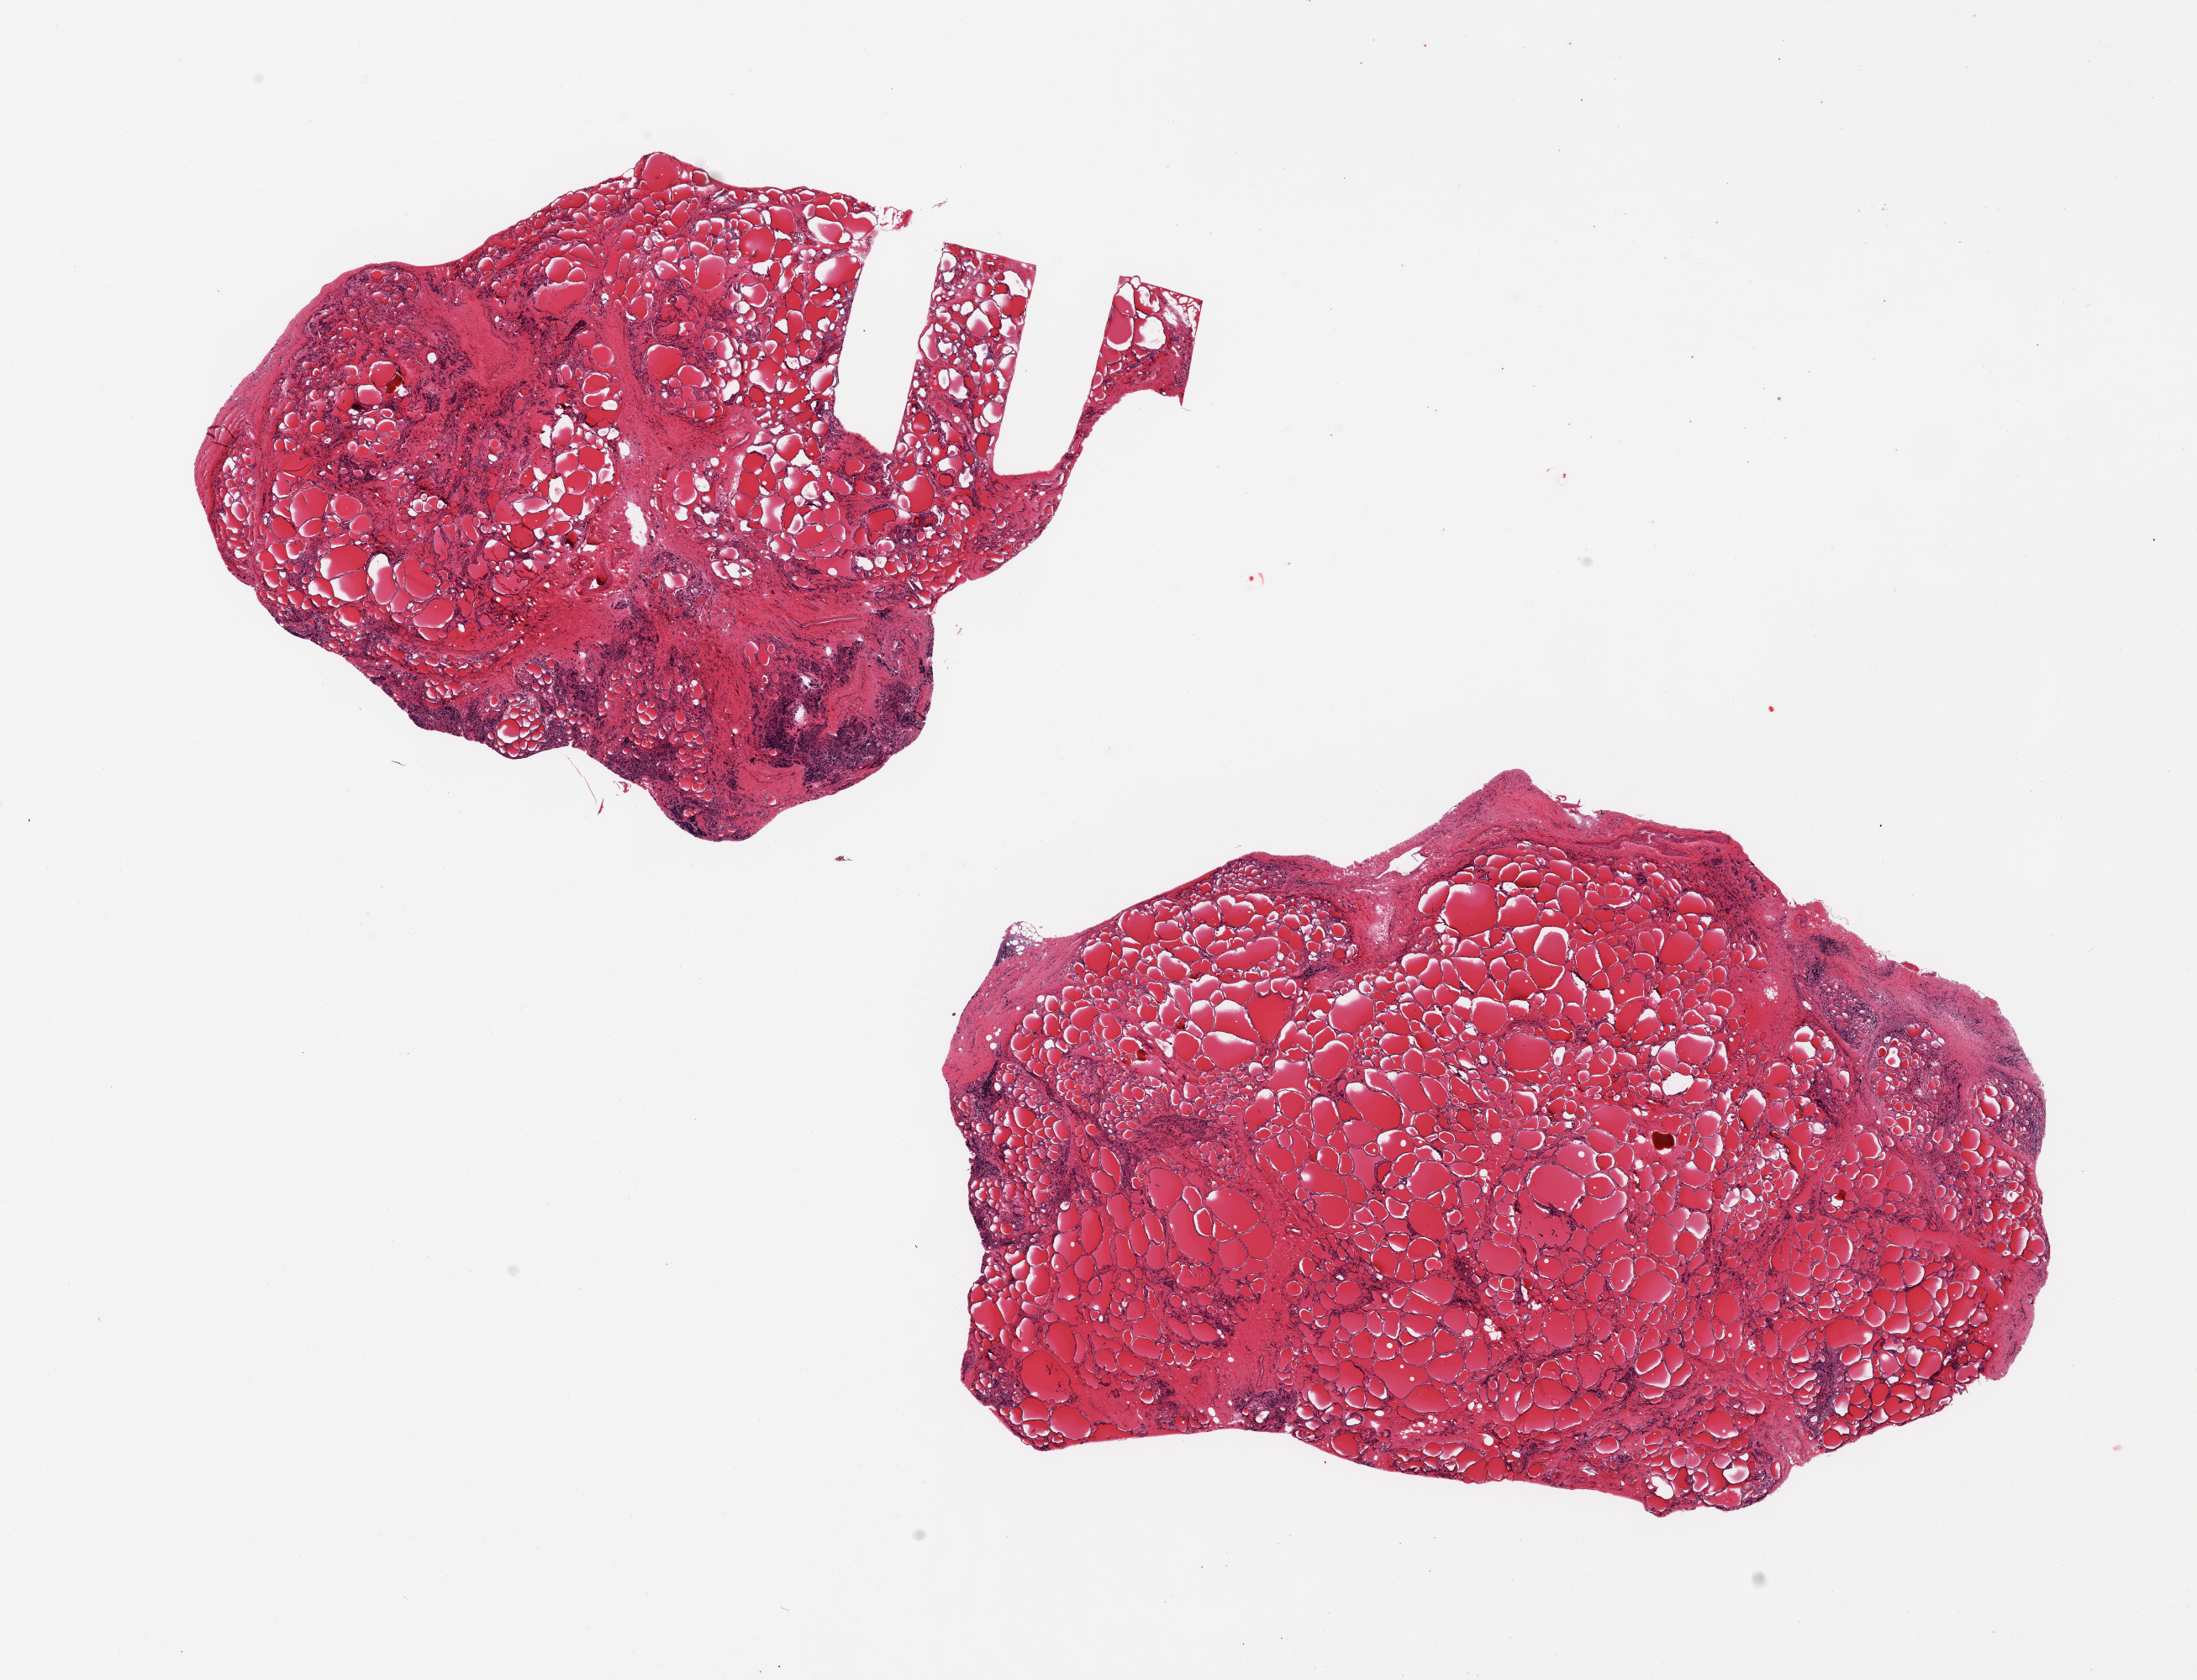
Haematoxylin and eosin whole-slide image, whole scanned area (about 20.7 x 15.8 mm, from a 20x scan) shown as a low-resolution overview. PAXgene-fixed paraffin-embedded (PFPE) section. Target tissue: thyroid. Tissue donor sample. Female donor.
Pathologist's review note for this sample: 2 pieces; interstitial fibrosis with nodularities and associated lymphocytic infiltration (Hashimoto's thyroiditis).